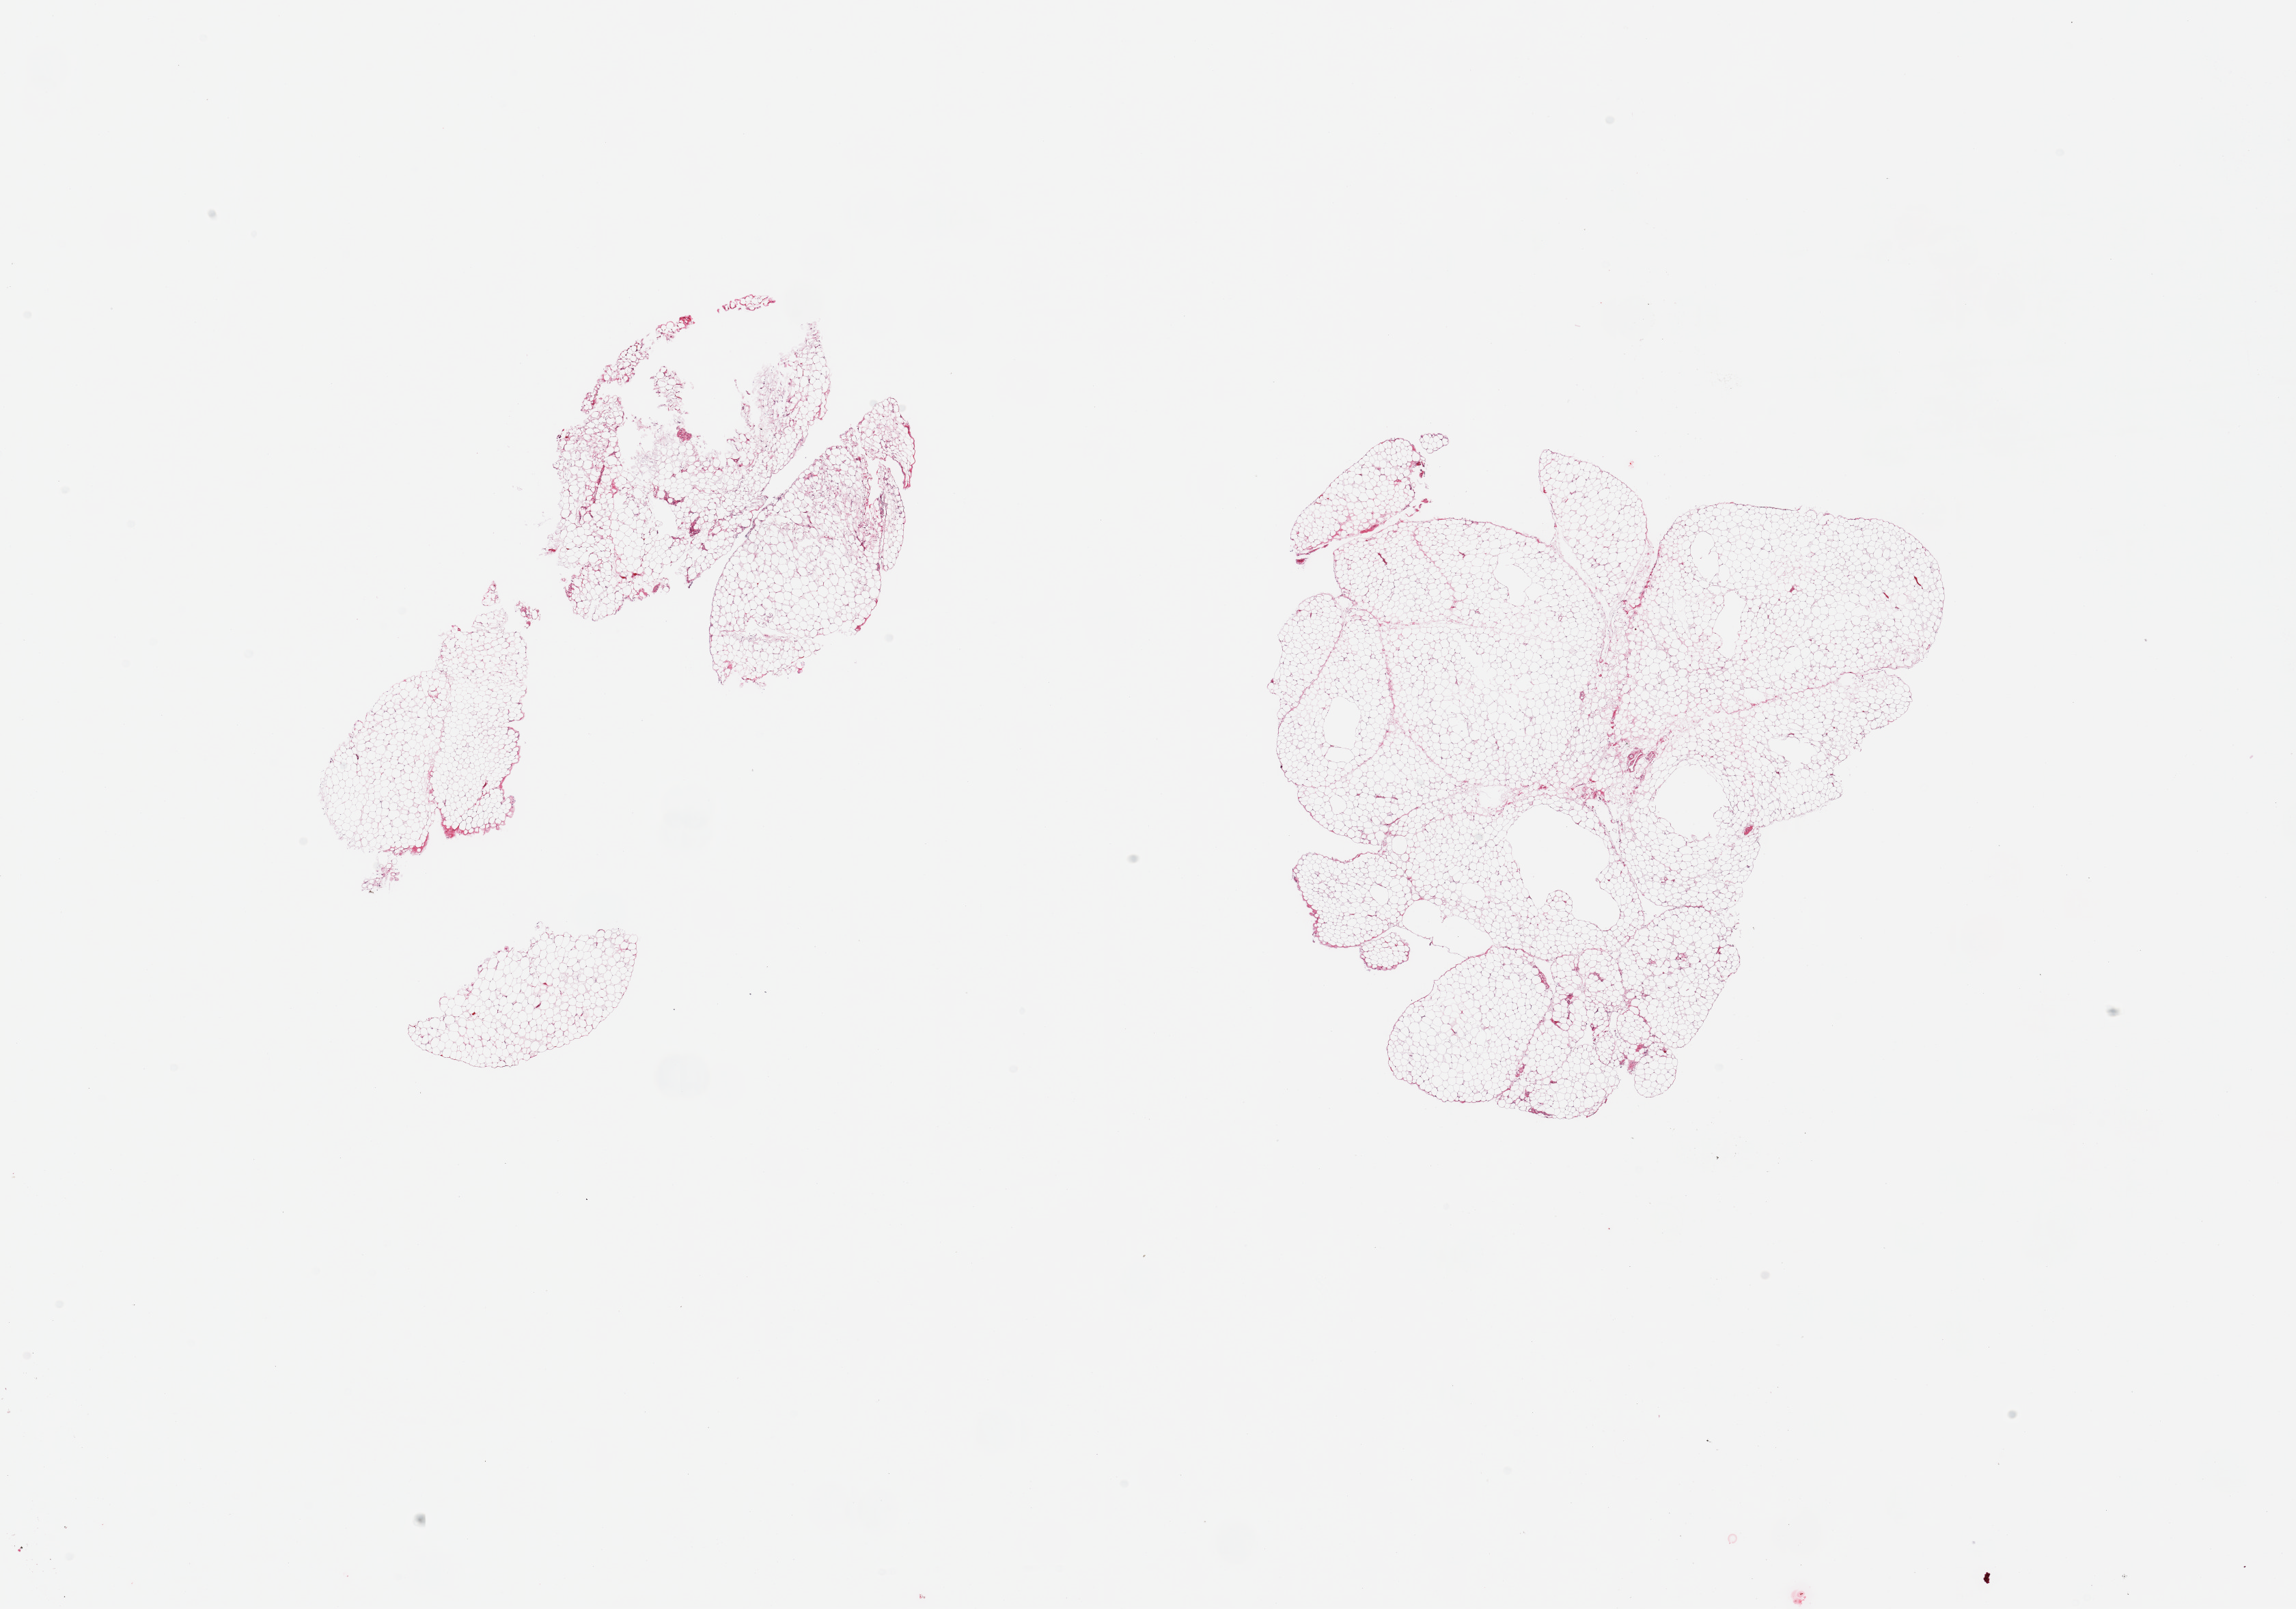
Hematoxylin and eosin (H&E) whole-slide image, brightfield, low-resolution overview of the scanned area, about 26.6 x 18.6 mm, PAXgene-fixed paraffin-embedded (PFPE) section, target tissue: omentum, tissue donor sample. Donor sex: male.
Reviewer comment on this tissue sample: 2 pieces; mature fat.